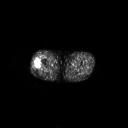
FDG PET of an extremity soft-tissue mass (from a PET/CT study), one axial slice; slice 233 of 267 in the series (ordered by position); 3.27 mm slice thickness; 128 × 128 image matrix. Patient: male, 43 years. From the clinical record (not read from this slice): histological type: poorly differentiated synovial sarcoma; grade: high; site of the primary tumour: right buttock.
Structures marked on this image (expert contour drawn on MRI and transferred to this co-registered scan by the dataset authors):
- gross tumour volume including surrounding oedema: box from (x=33, y=57) to (x=42, y=69) px
- gross tumour volume (mass): (x=34, y=59)–(x=42, y=69)